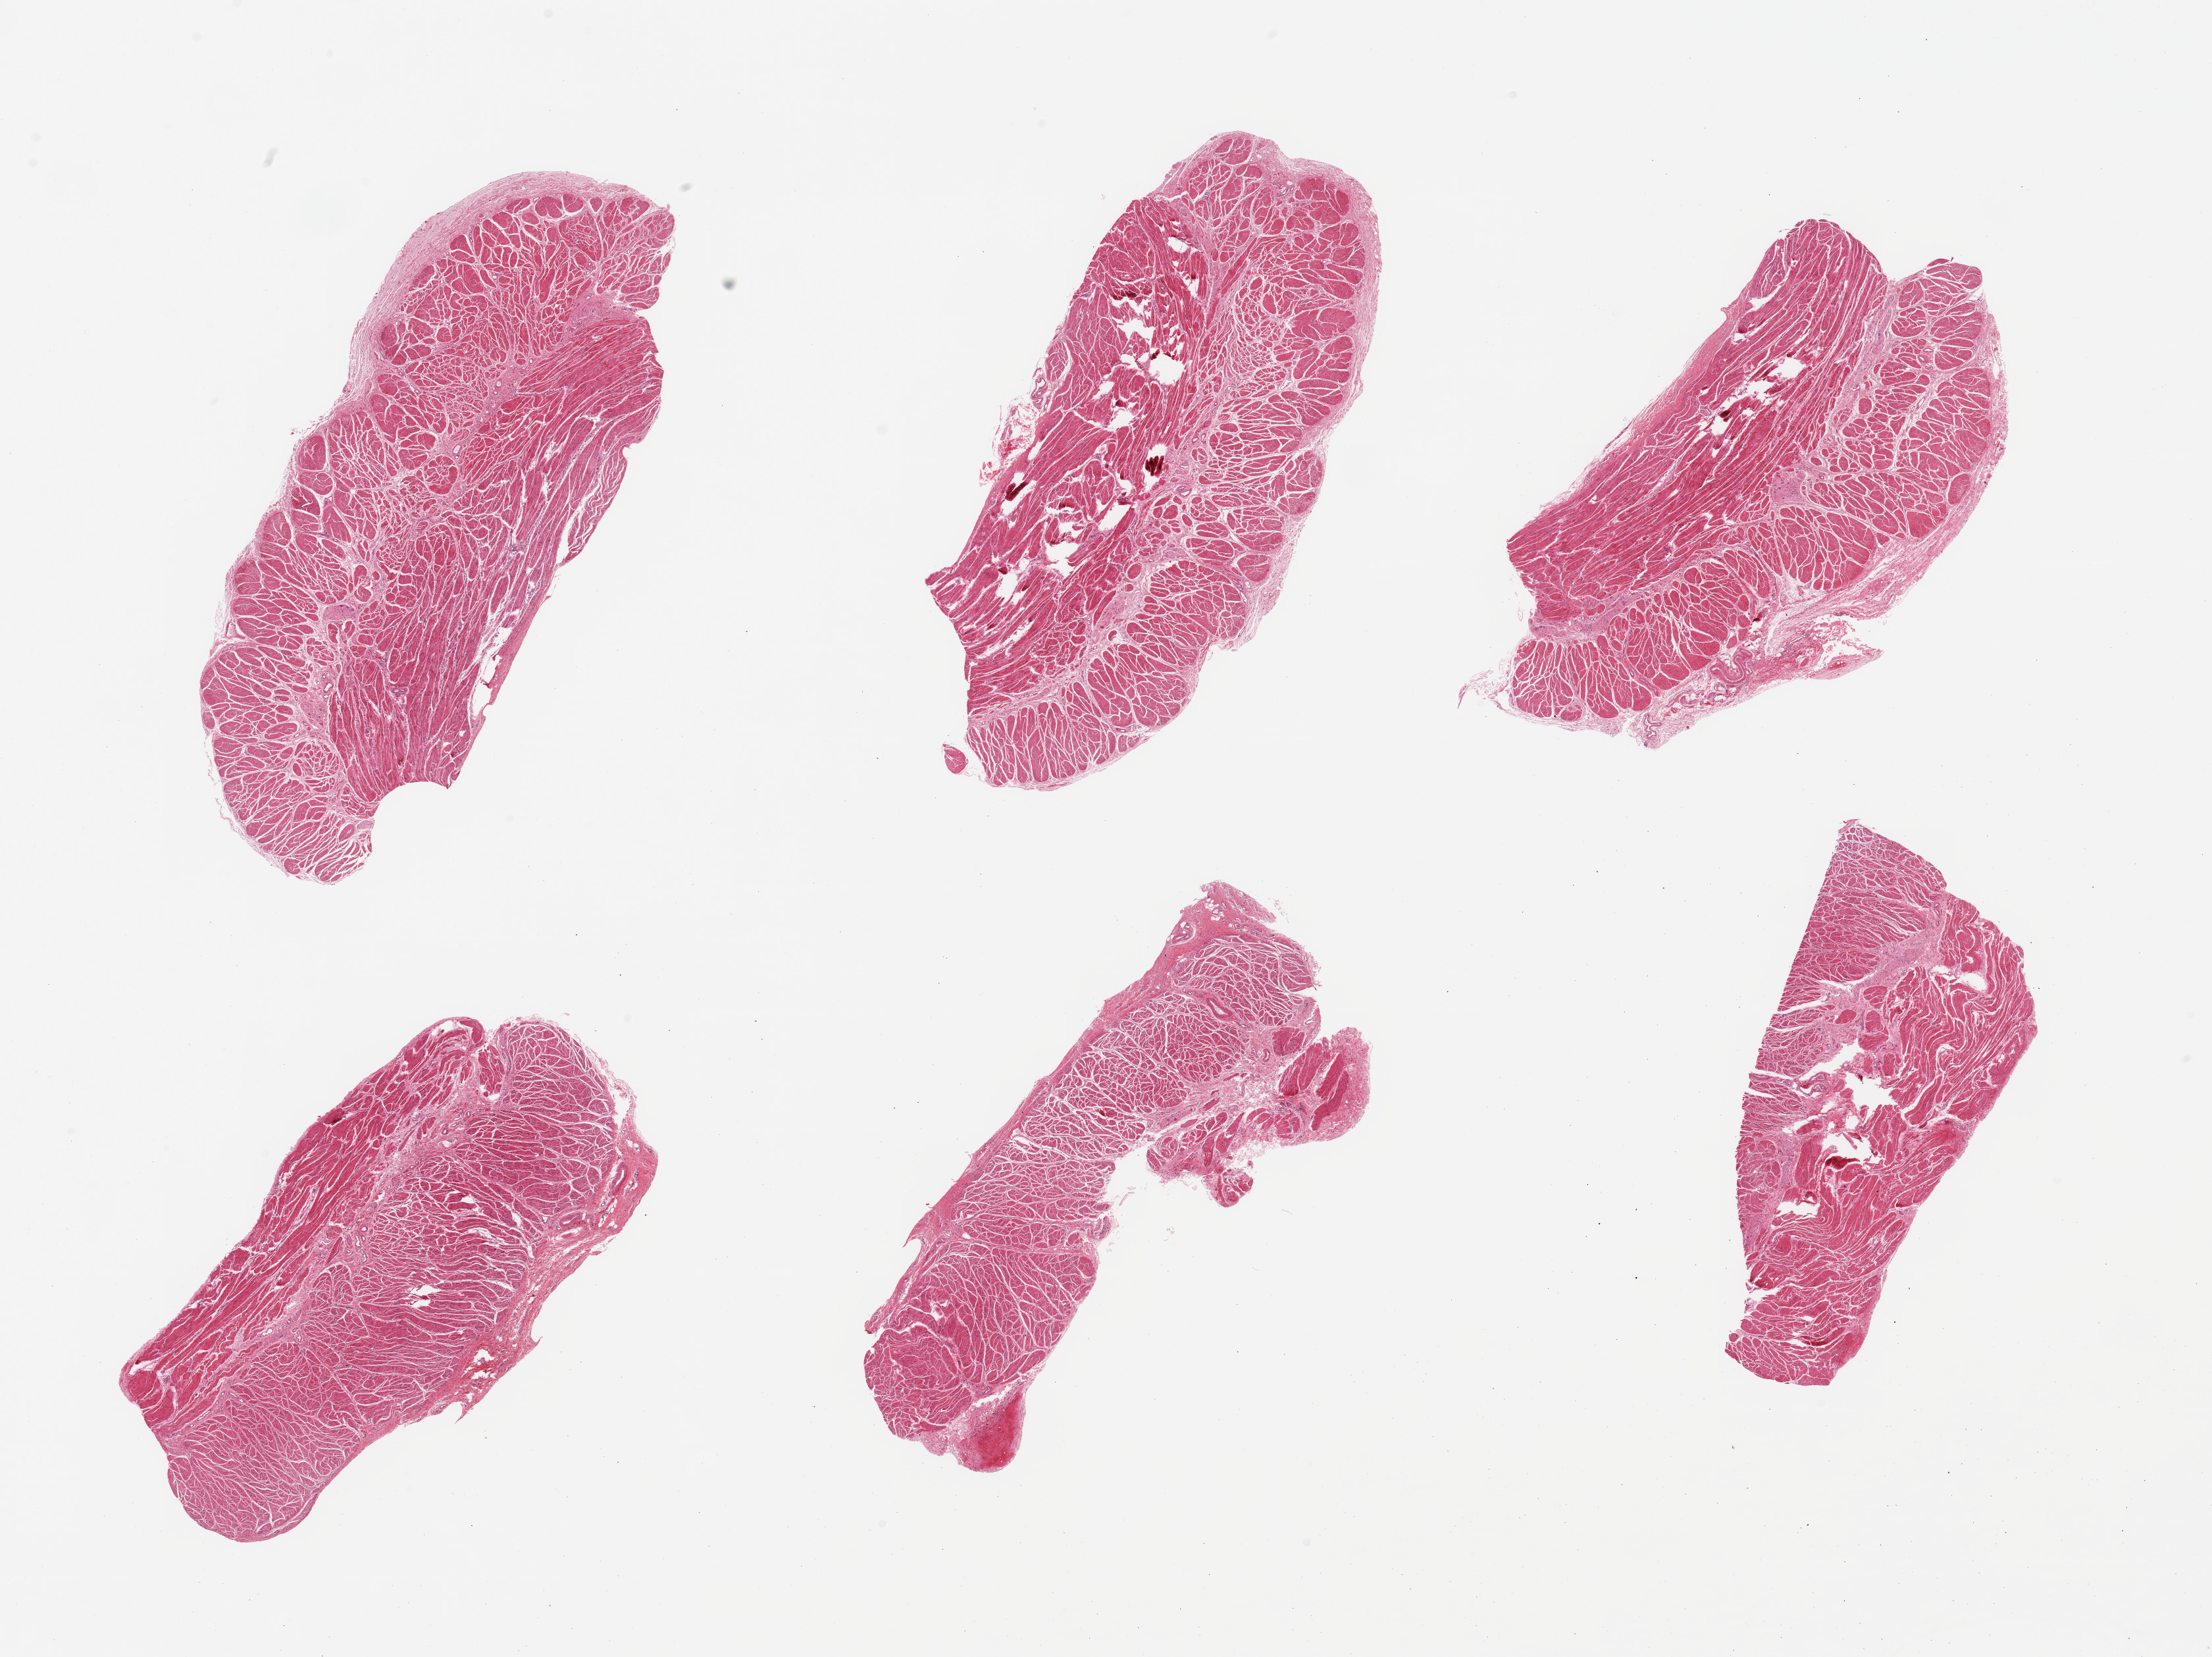
Digitized H&E-stained section — shown as a low-resolution overview of the whole scanned area (about 26.6 x 19.9 mm). PAXgene-fixed paraffin-embedded (PFPE) section. Sampled site (target tissue): gastroesophageal junction. Tissue donor sample.
* pathologist's review note for this sample: 6 pieces; target muscularis